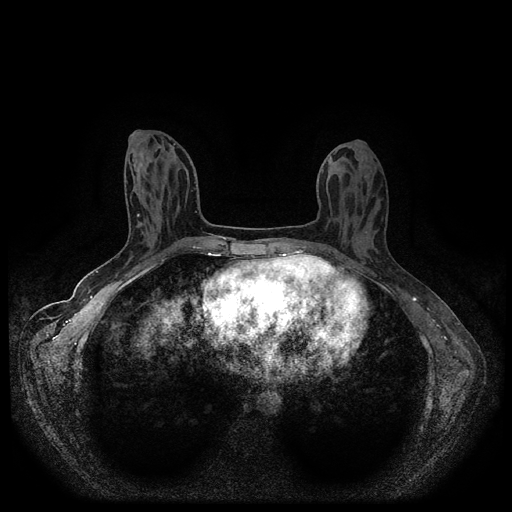
Breast MRI (dynamic contrast-enhanced, multi-phase), one axial slice; position 39 of 116 along the scan axis; dynamic contrast-enhanced series, time point 2 of 5 at this slice position (early post-contrast); 1.5 T; TE 2.6 ms, TR 5.4 ms; 2 mm slice thickness; 512 × 512 image matrix, field of view 340 × 340 mm. Female patient, age 30 years.
Structures marked on this image (semi-automatic segmentation, software-assisted and operator-edited):
- breast lesion (labelled benign in the annotation): bounding box (x1, y1, x2, y2) in pixels: (355, 236, 368, 248)